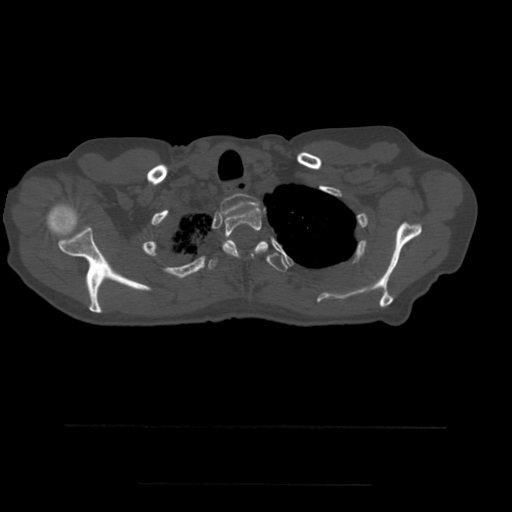
CT including the spine, one axial slice; slice 431 of 544 in the series (ordered by position); bone window (W 1800 / L 400 HU); 1.25 mm slice thickness; 512 × 512 image matrix, field of view 350 × 350 mm. Patient age 58 years. Case-level facts recorded for this patient, not image findings: primary cancer: lung.
Structures marked on this image (semi-automatic segmentation, software-assisted and operator-edited):
- T1 vertebra: bounding box [x1, y1, x2, y2] px = [221, 194, 261, 215]
- T2 vertebra: [223, 205, 268, 258]
- T3 vertebra: [208, 241, 289, 273]